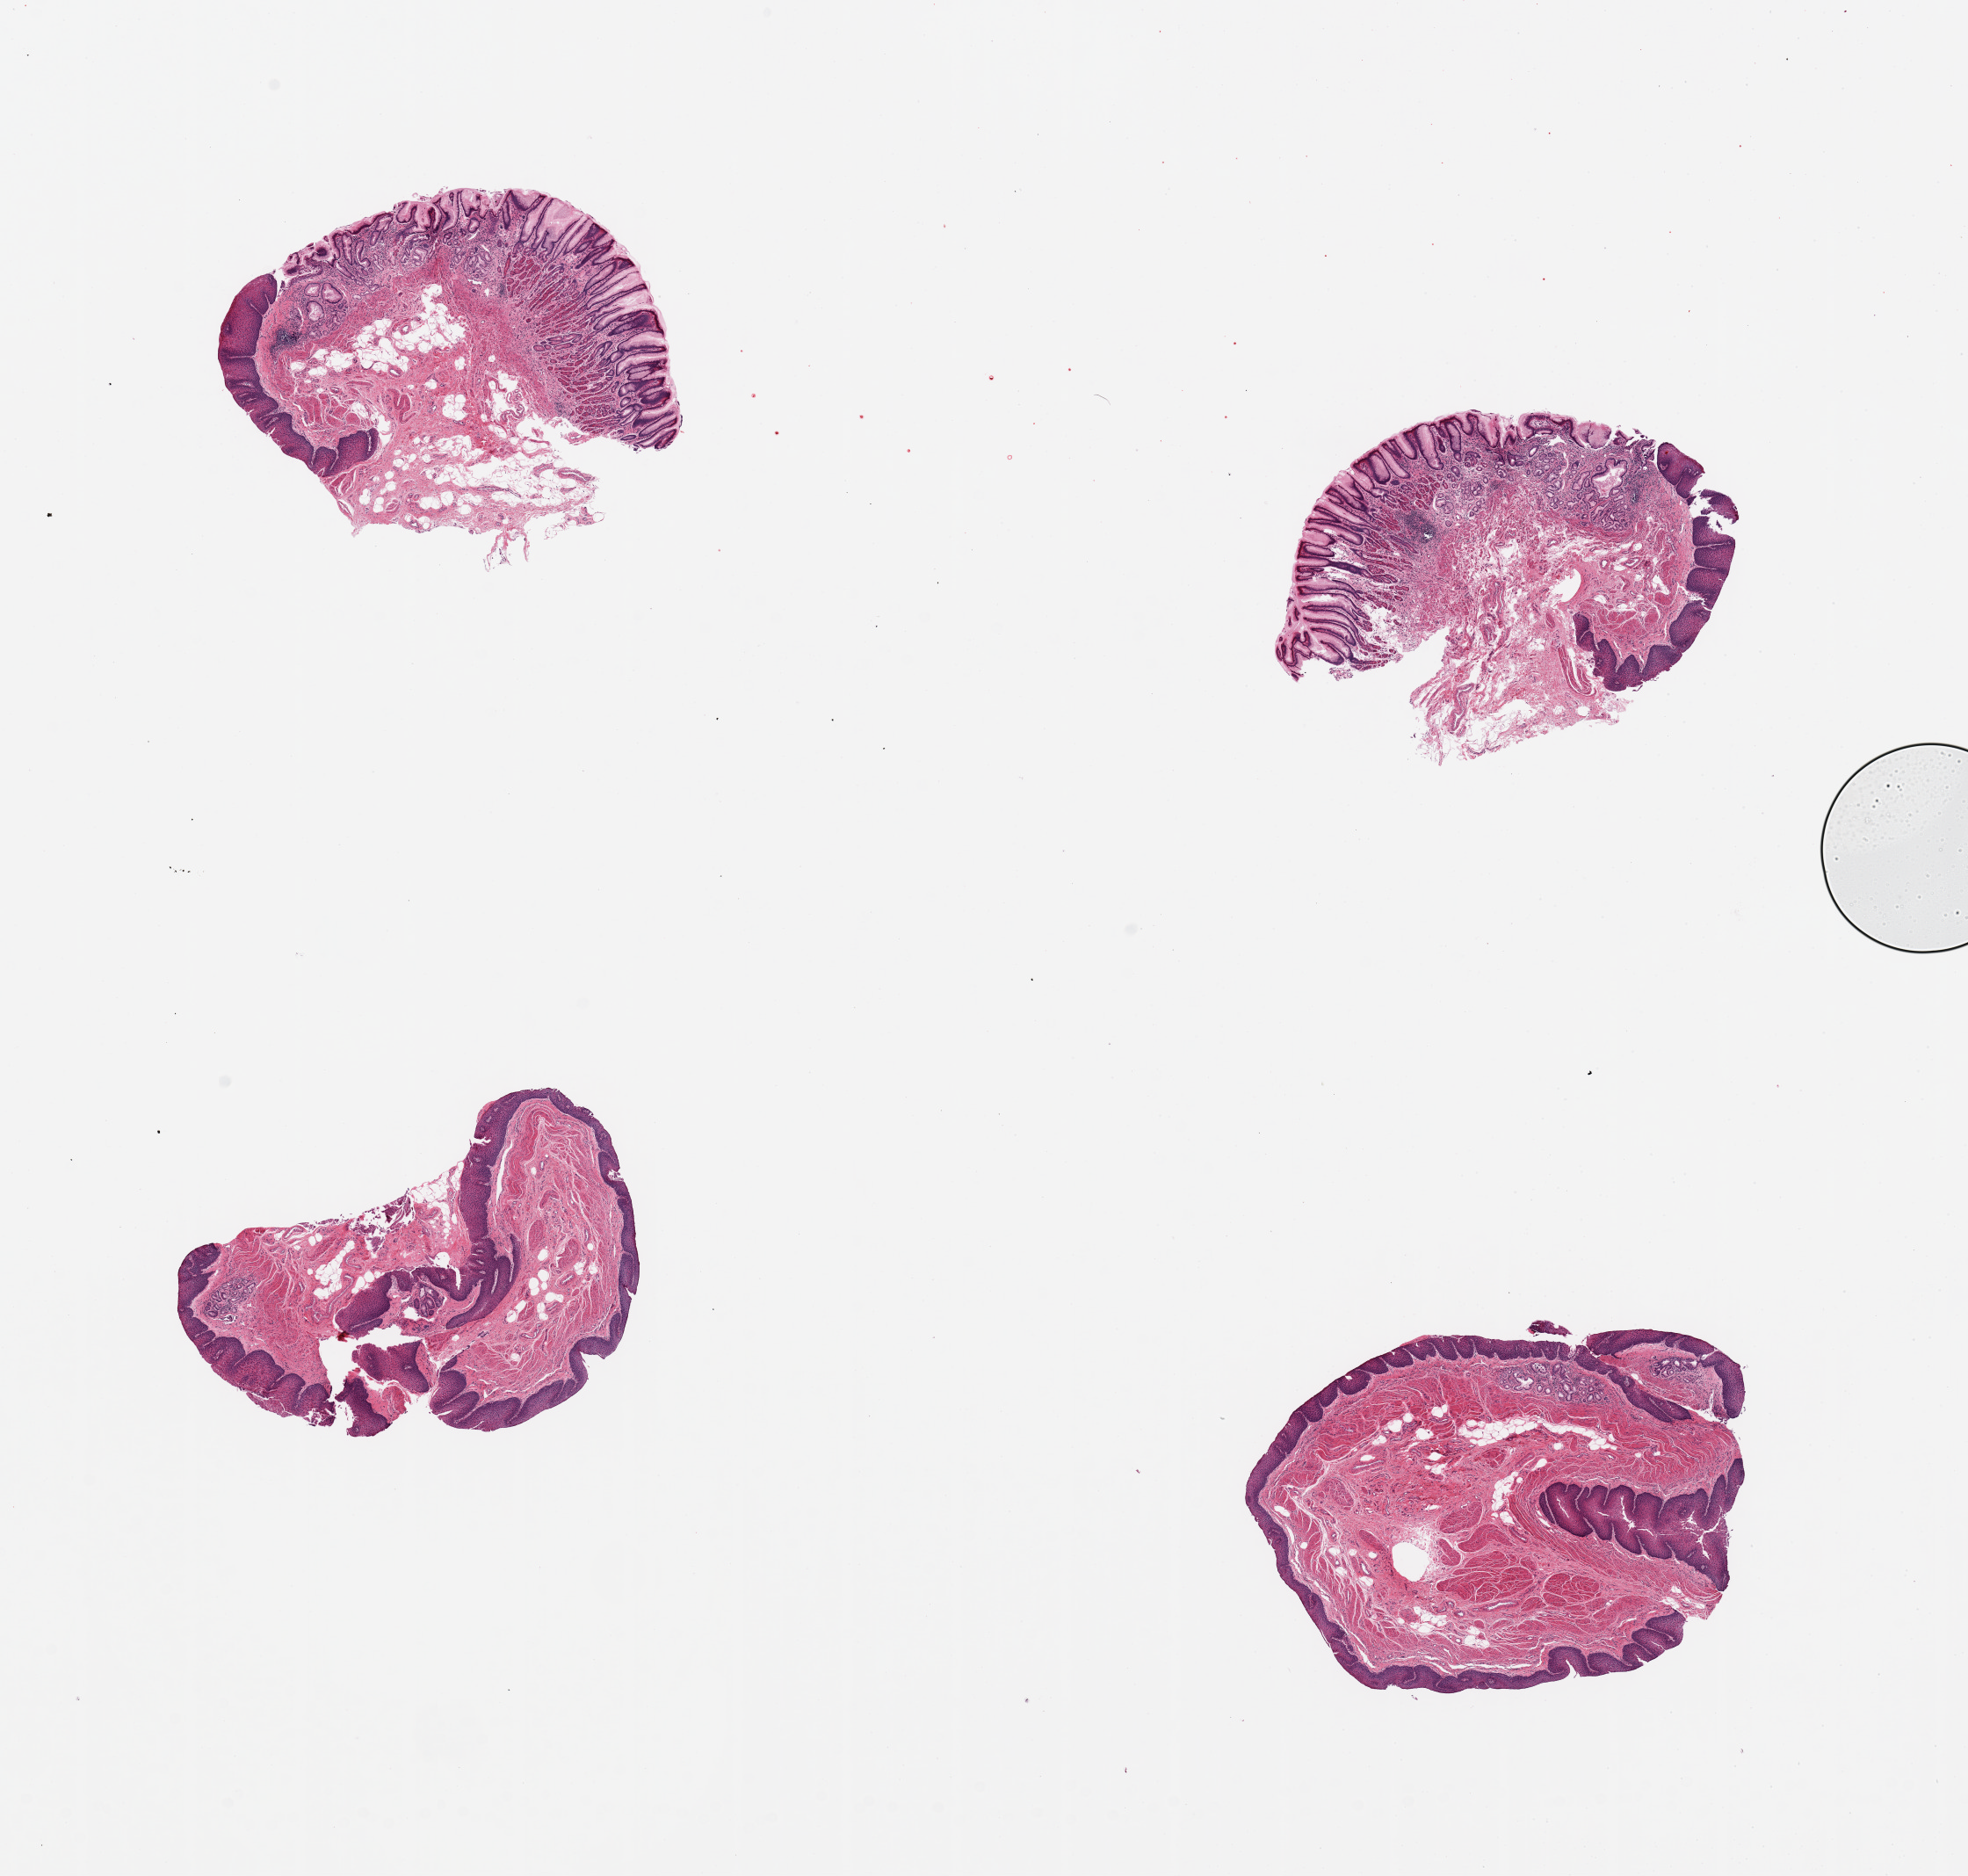
Haematoxylin and eosin whole-slide image — shown as a low-resolution overview of the whole scanned area (about 17.7 x 16.9 mm, acquisition: 20x scan), PAXgene-fixed, paraffin-embedded tissue, sampled site (target tissue): esophageal mucous membrane, tissue donor sample. Female donor.
Pathologist's review note for this sample: 4 pieces, 2 include glandular mucosa of gastroesophageal junction (NOT TARGET).